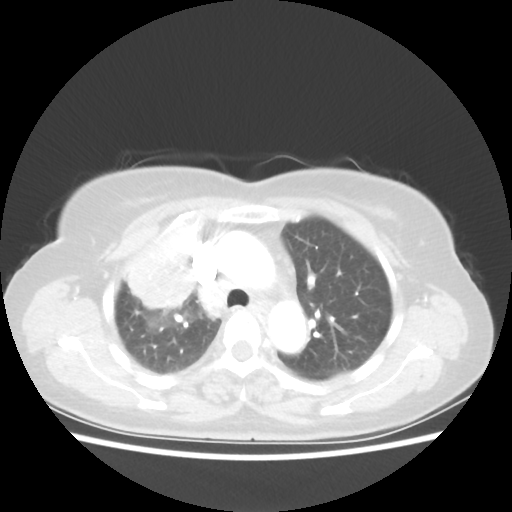
Chest CT, one axial slice. Slice 38 of 55 in the series (ordered by position). Reconstruction kernel STANDARD. 80 kVp. Lung window (W 1500 / L -600 HU). 512 × 512 image matrix, field of view 337 × 337 mm. Patient: female, 62 years. From the clinical record (not read from this slice): clinical TNM (as recorded): T4 N3 M0.
Outlined on this slice (bounding box drawn by a radiologist):
- lung tumour (recorded histology: squamous cell carcinoma): bounding box <116,206,213,311> (left, top, right, bottom; pixels)